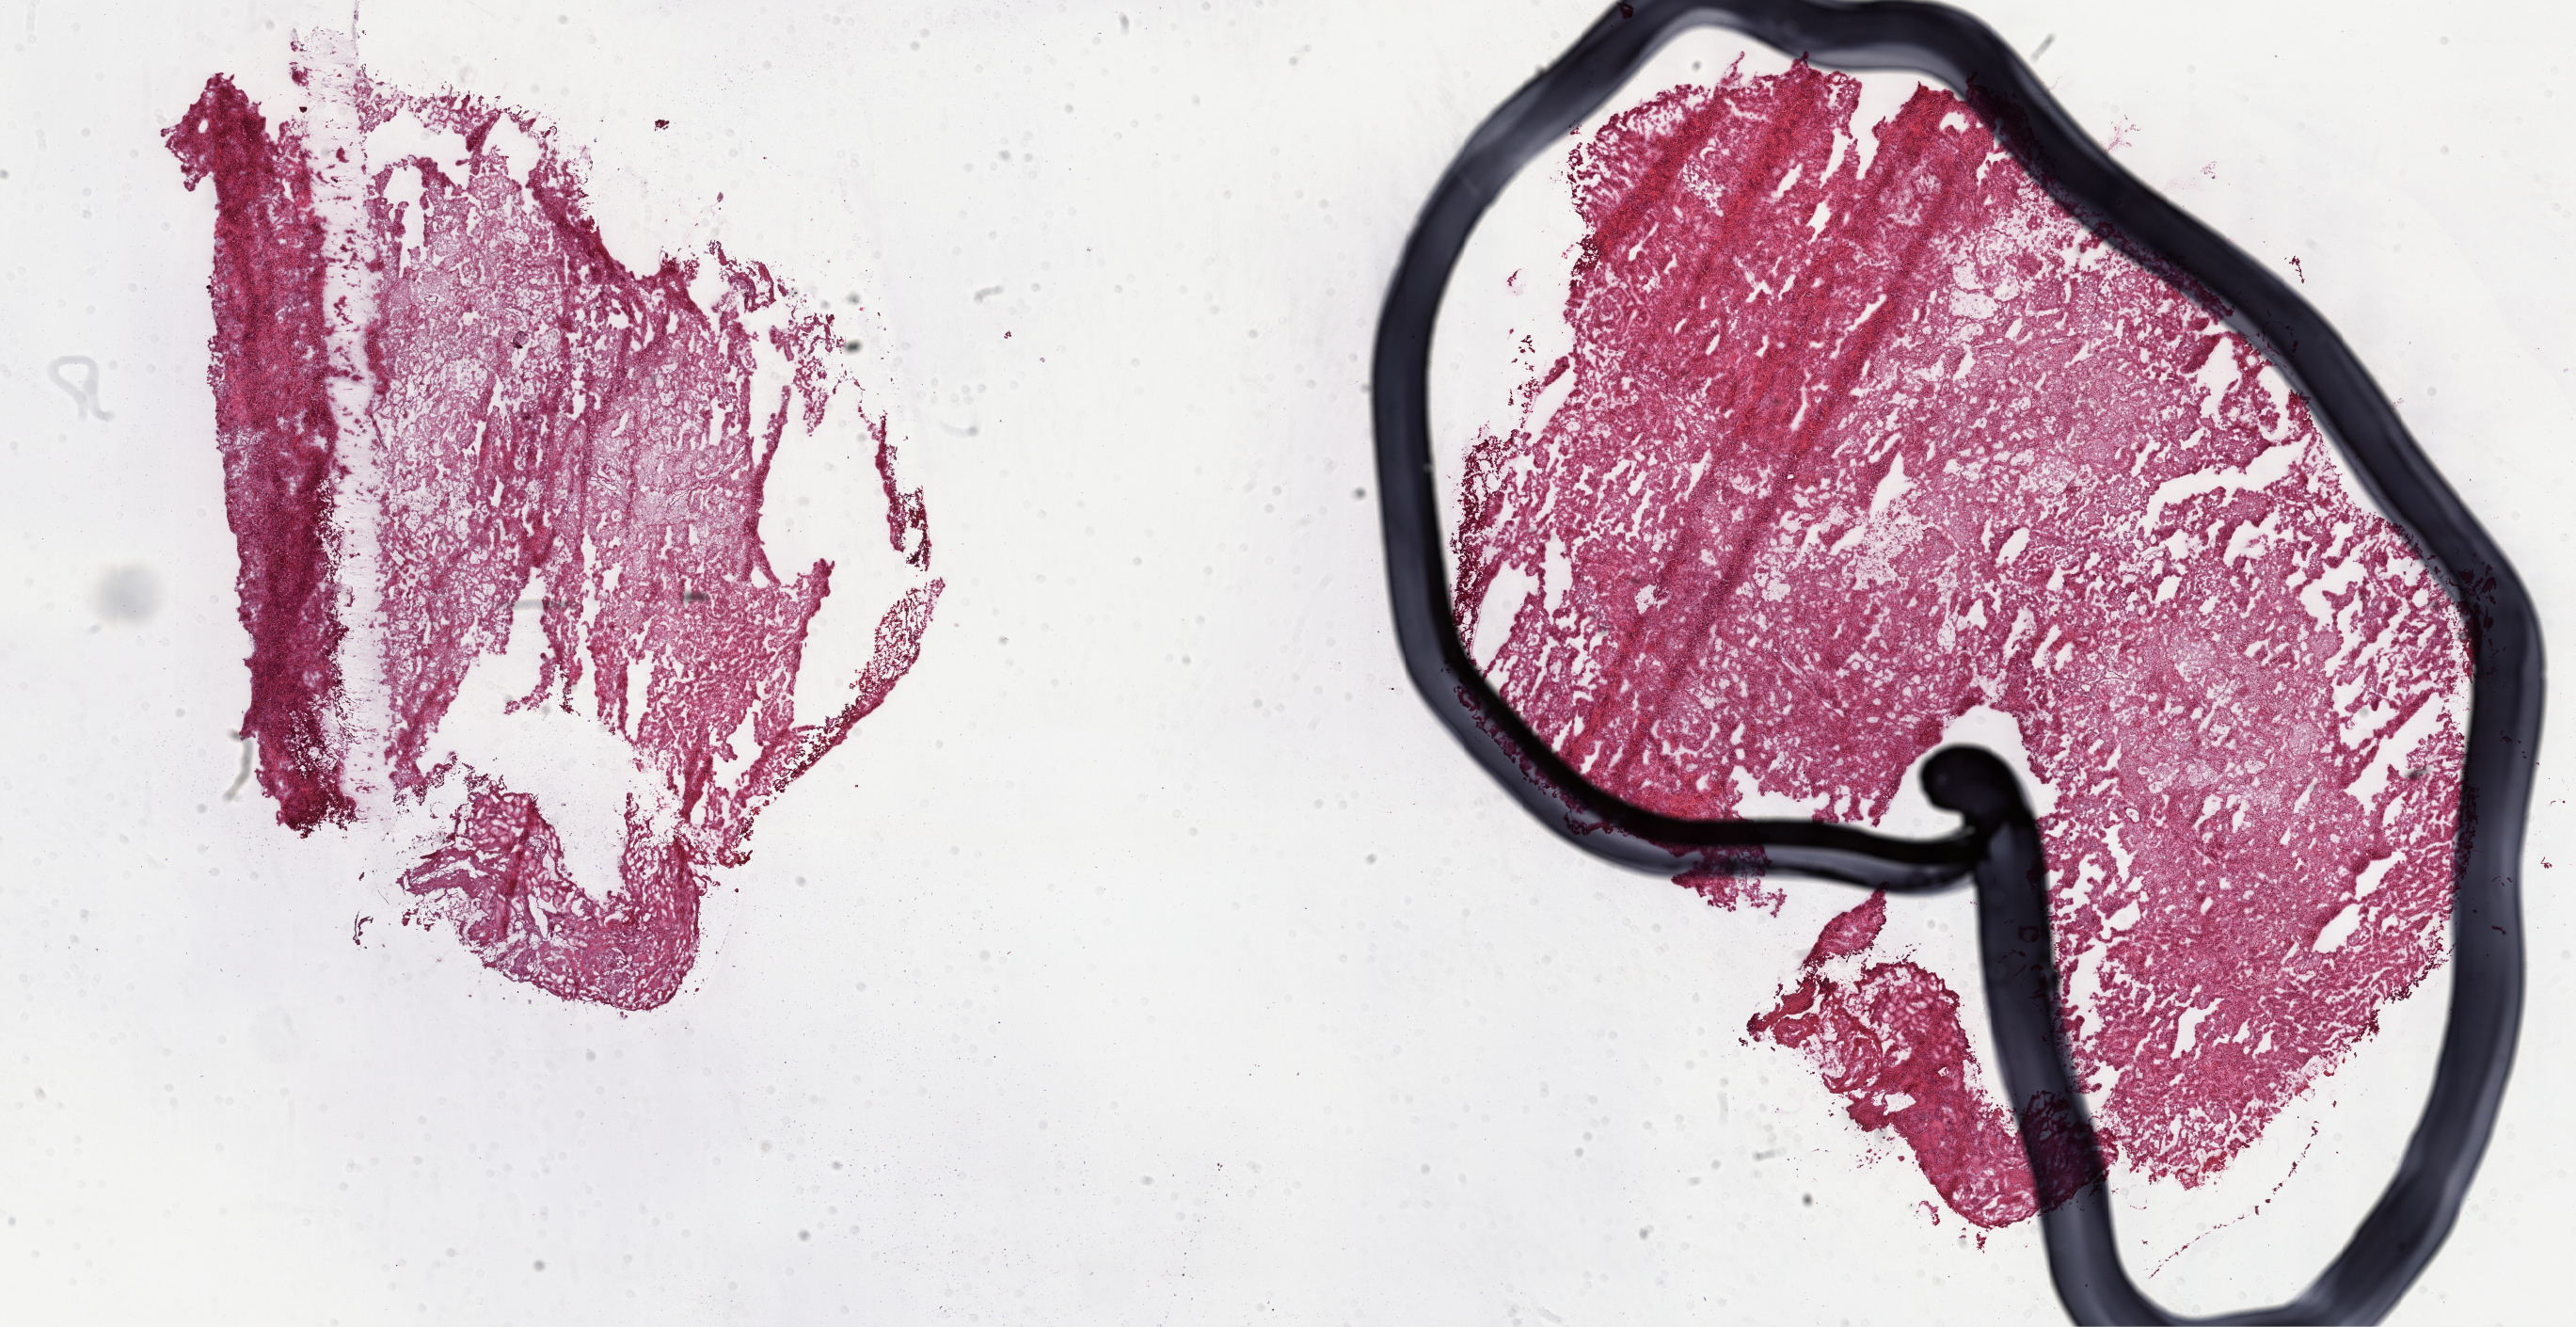
Digitized H&E-stained tissue section (whole slide) — shown as a low-resolution overview of the whole scanned area (about 22.1 x 11.4 mm, from a 40x scan); frozen section from the top of the tissue portion; kidney, primary tumour sample. Female patient; age at initial diagnosis 51 years. Pathologist review of this section (percent, as recorded): tumour cells 100%, tumour nuclei 70%.
Diagnosis: Papillary adenocarcinoma, NOS.